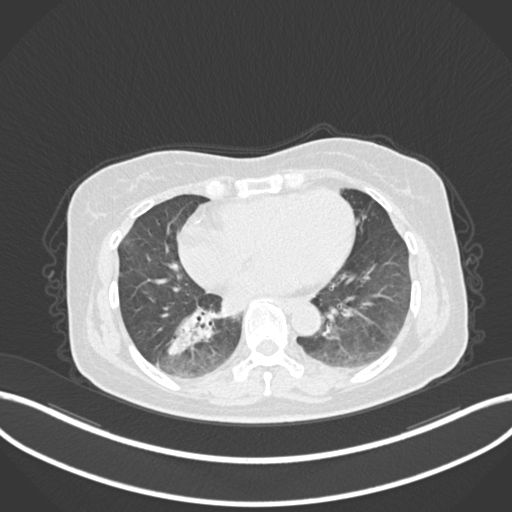
Chest CT, one axial slice; position 55 of 222 along the scan axis; reconstruction kernel B30f; 120 kVp; lung window (W 1500 / L -600 HU); 1 mm slice thickness; 512 × 512 image matrix, field of view 400 × 400 mm. Patient: female, 67 years. Case-level facts recorded for this patient, not image findings: clinical TNM (as recorded): T1c N1 M0; histopathological grade: G2-3.
Structures marked on this image (bounding box drawn by a radiologist):
- lung tumour (recorded histology: adenocarcinoma): box from (x=167, y=297) to (x=219, y=365) px